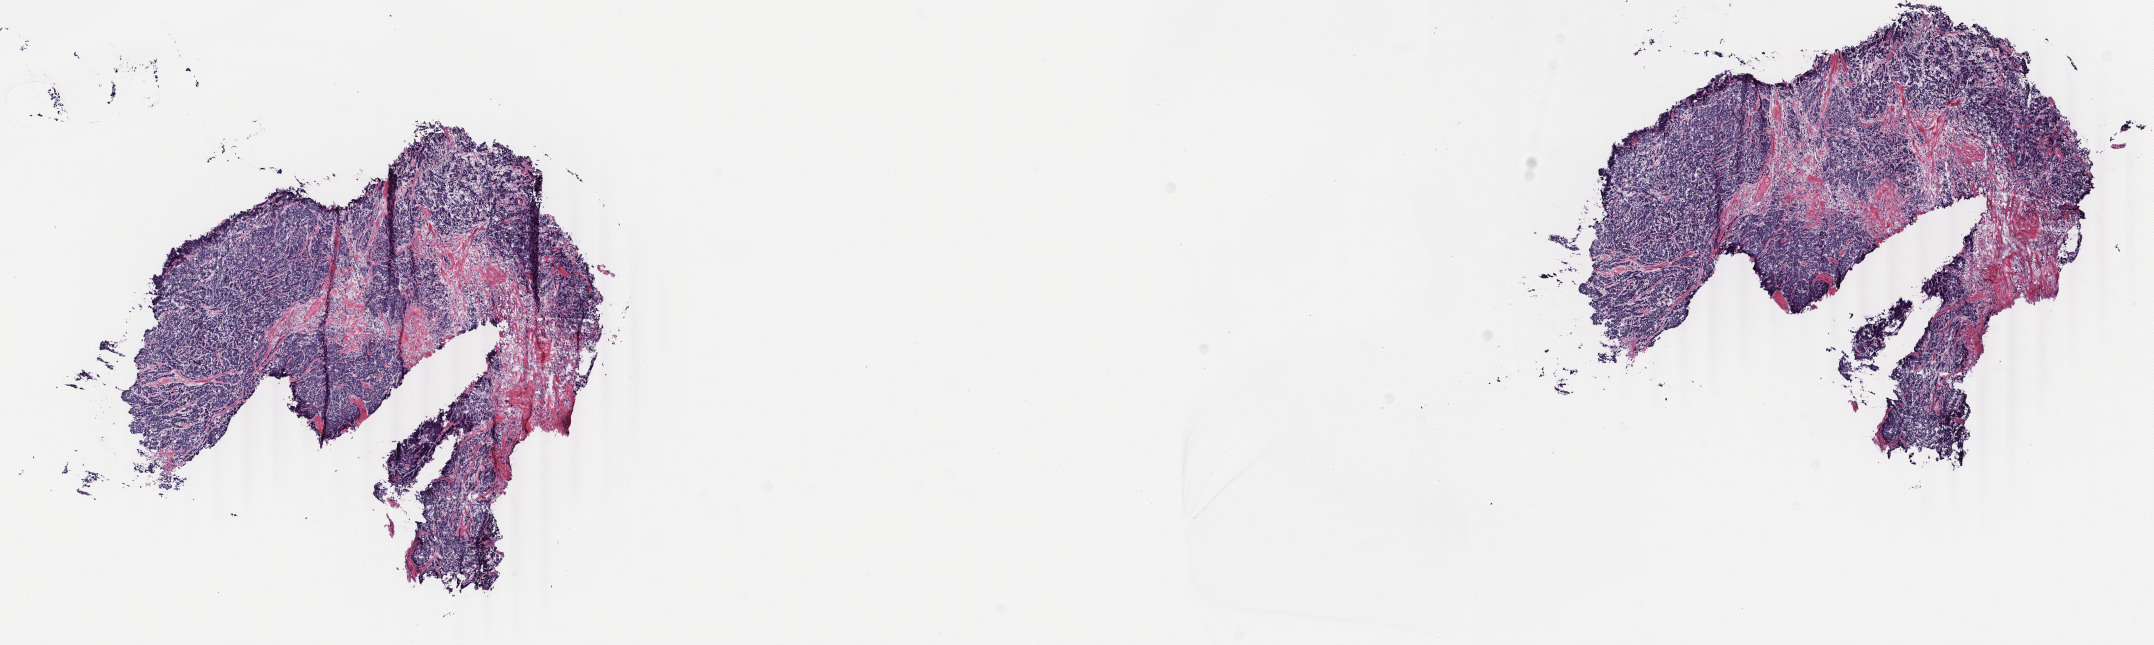
Digitized Hematoxylin and eosin (H&E) stained tissue section (whole slide) — a low-resolution overview of the entire scanned area, about 17.1 x 5.1 mm (acquisition: 40x scan), frozen section from the bottom of the tissue portion, primary tumour sample from the breast. Female patient; age at initial diagnosis 47 years. Slide review estimates, as recorded: tumour cells 90%, tumour nuclei 85%, normal cells 0%, stromal cells 10%, necrosis 0%. Infiltration values recorded for this section: lymphocyte infiltration 0%, monocyte infiltration 0%, neutrophil infiltration 0%.
Lymph nodes positive (case pathology): 4 of 16 examined. Histologic diagnosis: Infiltrating duct carcinoma, NOS. AJCC pathologic stage: IIIA.